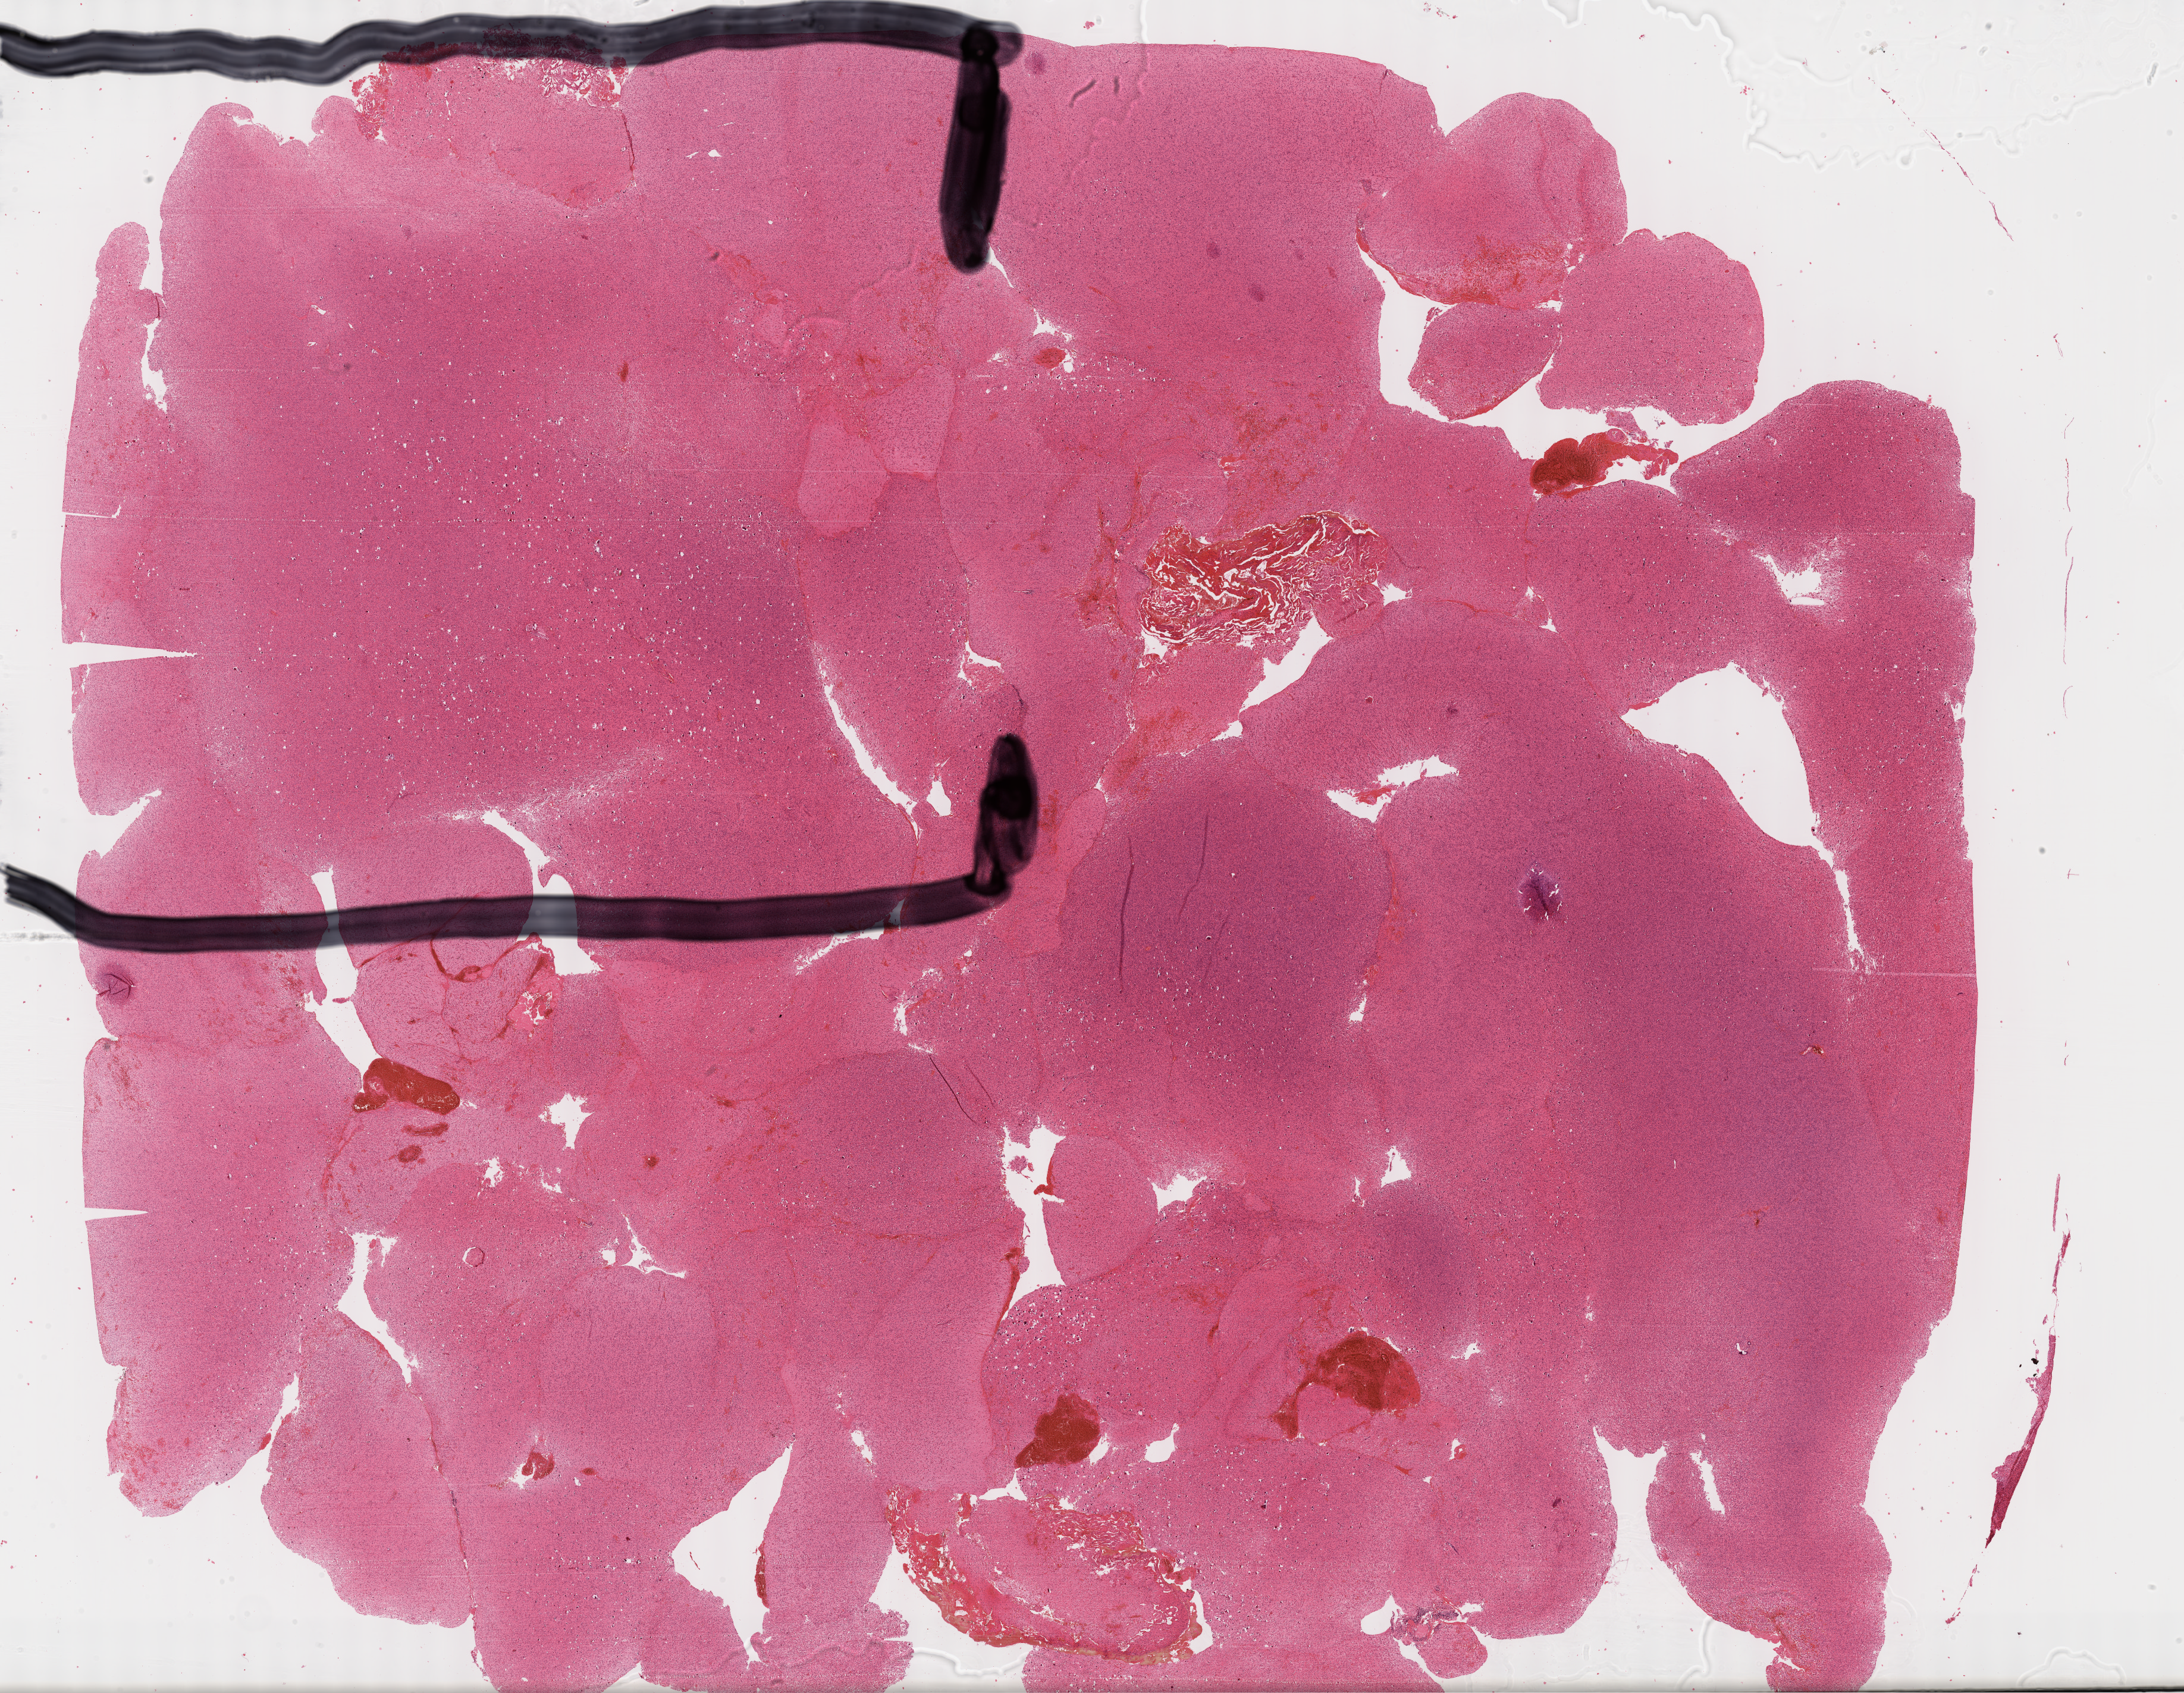
H&E-stained whole-slide image, whole scanned area (about 29.7 x 23.0 mm, acquisition: 40x scan) shown as a low-resolution overview. Formalin-fixed paraffin-embedded (FFPE) diagnostic section. Brain, primary tumour sample. Patient: male, age at initial diagnosis 46 years.
Pathologic diagnosis: Astrocytoma, anaplastic (cerebrum).